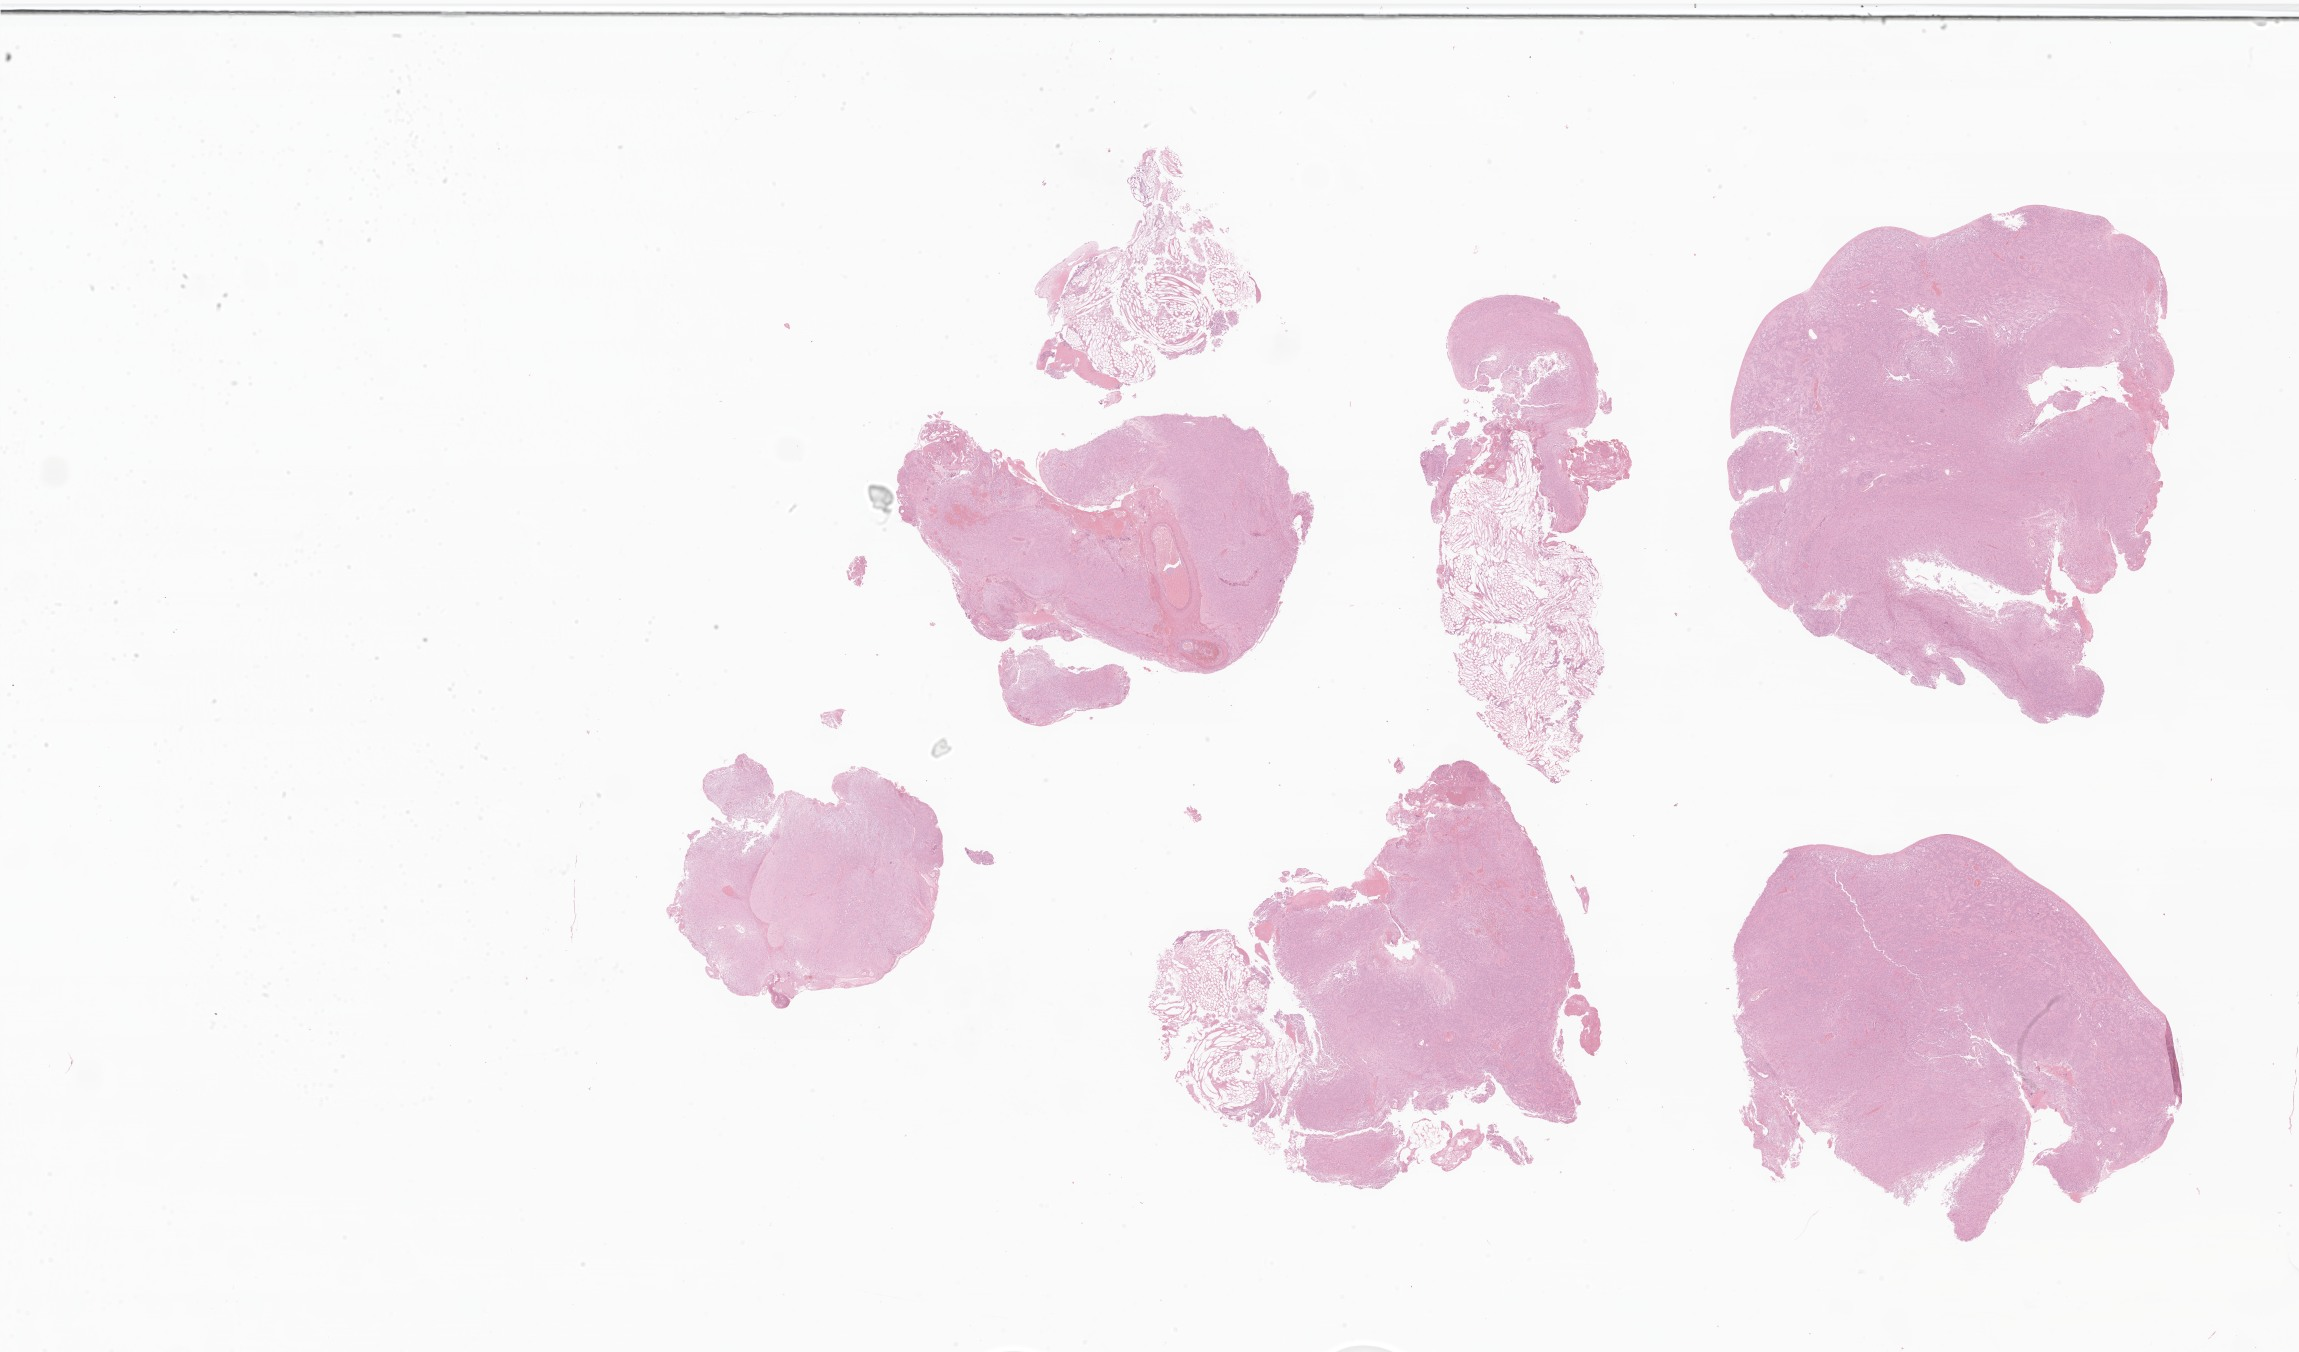
H&E whole-slide image of tumor tissue from the brain — whole scanned area (about 38.8 x 22.8 mm) shown as a low-resolution overview; formalin-fixed, paraffin-embedded (FFPE) tissue. Female patient, age 68 months (5 years 8 months).
Diagnosis (ICD-O-3 morphology term): Ependymoma, anaplastic.